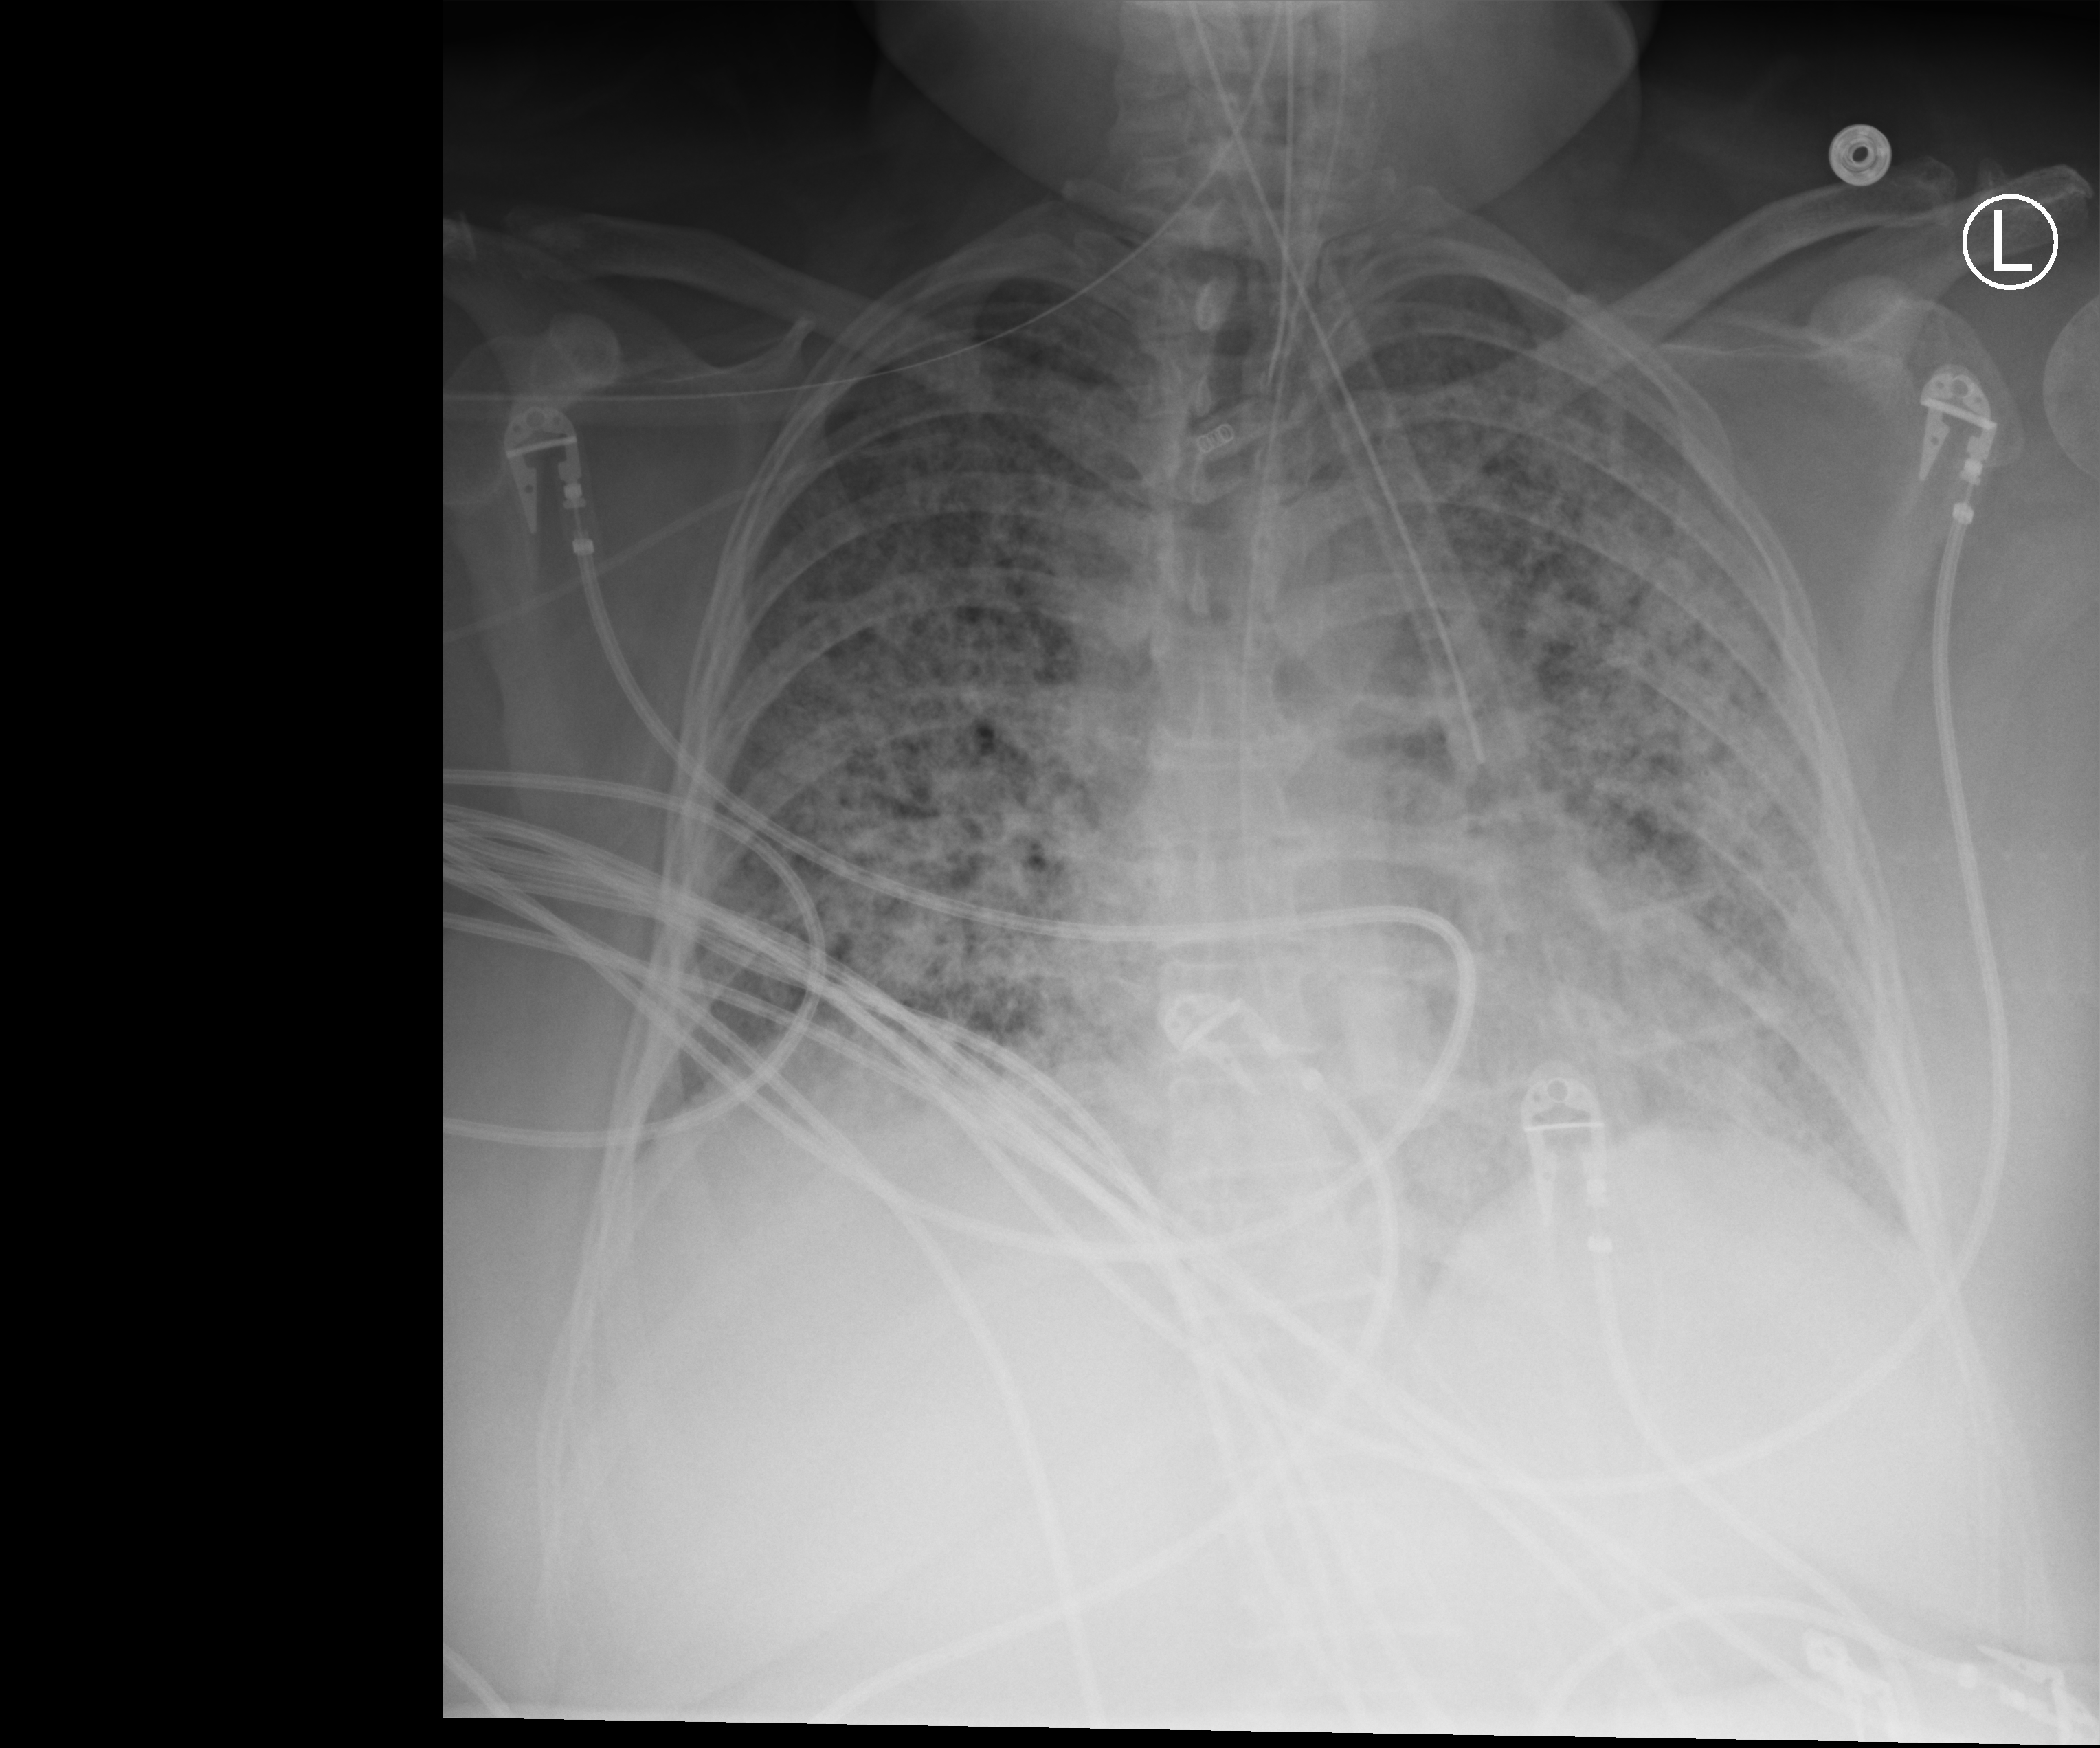
Portable chest radiograph; anteroposterior (AP) projection. Patient hospitalised with COVID-19; female, aged 18–59 years.
From the hospital-stay record, not from the radiograph (when in the stay this image was taken is not recorded): admitted to intensive care during this hospital stay: yes; length of hospital stay: 95 days.